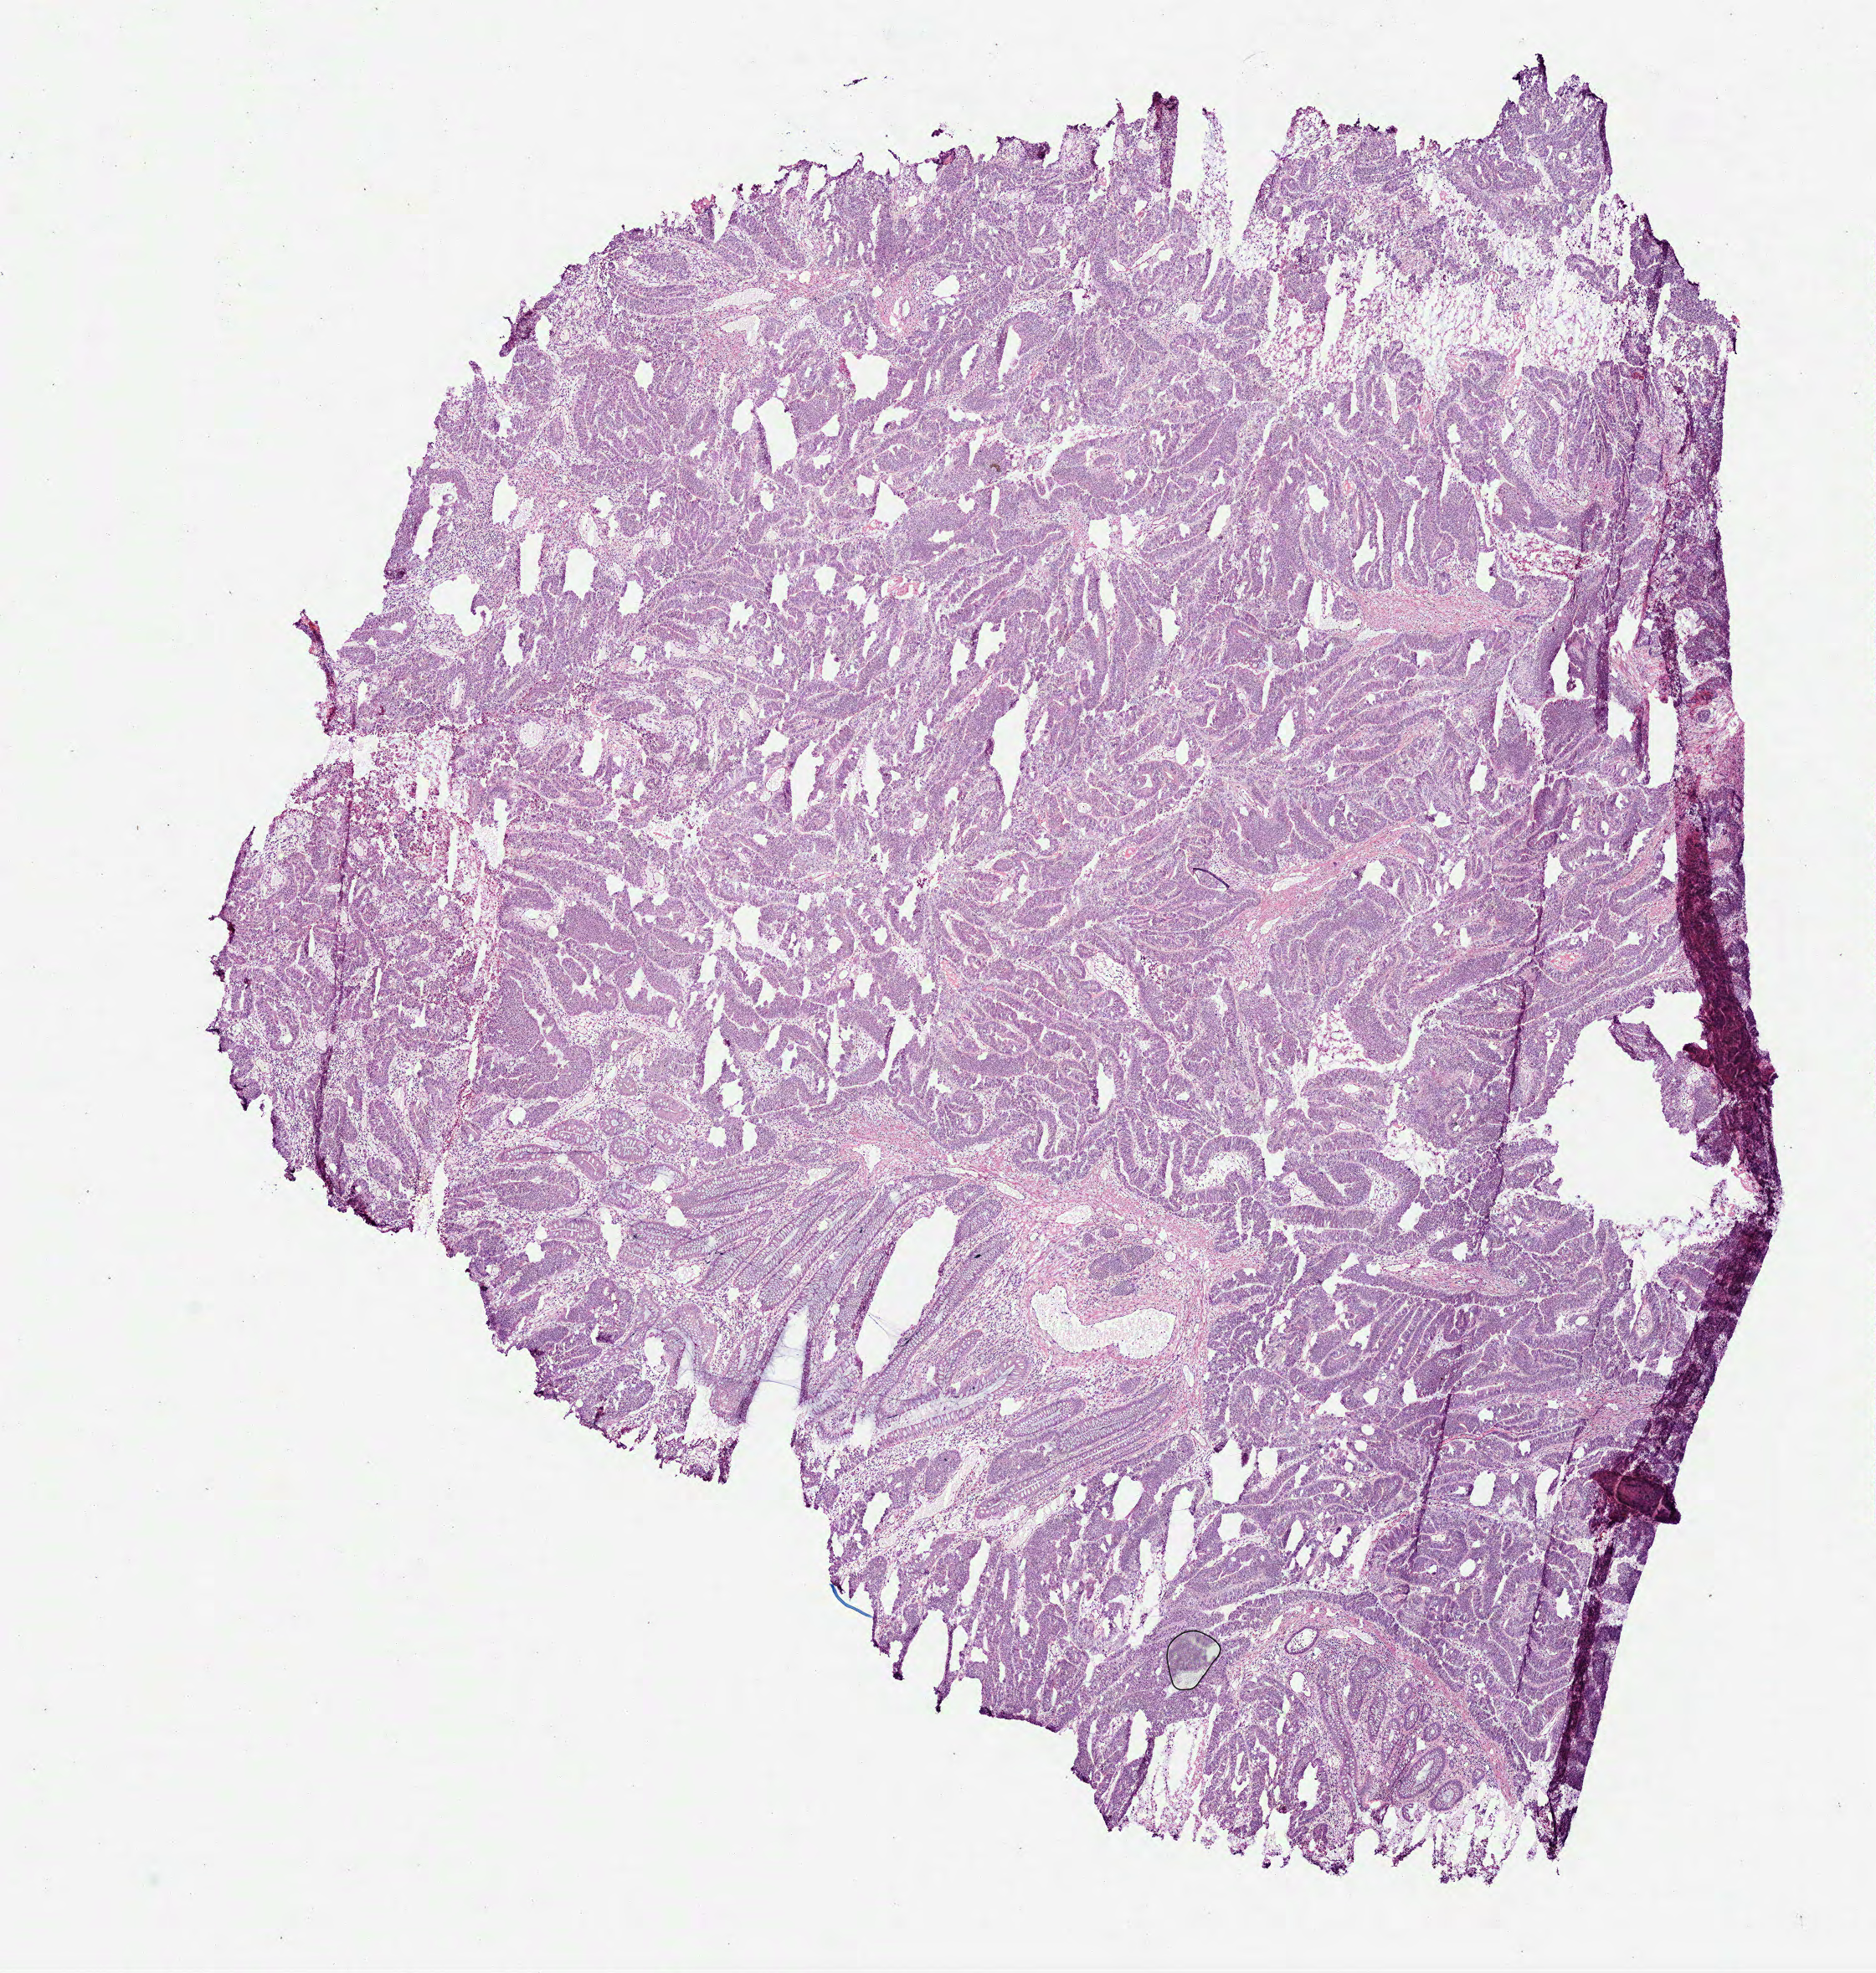
Digitized Hematoxylin and eosin (H&E) stained tissue section (whole slide), whole scanned area (about 9.0 x 9.5 mm, from a 40x scan) shown as a low-resolution overview, frozen section from the bottom of the tissue portion, sample: primary tumour, rectum. Patient: male, age at initial diagnosis 43 years. Composition of this section per pathologist review: tumour cells 77%, tumour nuclei 80%, normal cells 8%, stromal cells 10%, necrosis 5%.
Lymph nodes positive (case pathology): 18 of 37 examined. TNM: T4a N2b MX. Pathologic diagnosis: Adenocarcinoma, NOS (rectosigmoid junction). AJCC pathologic stage: IV.